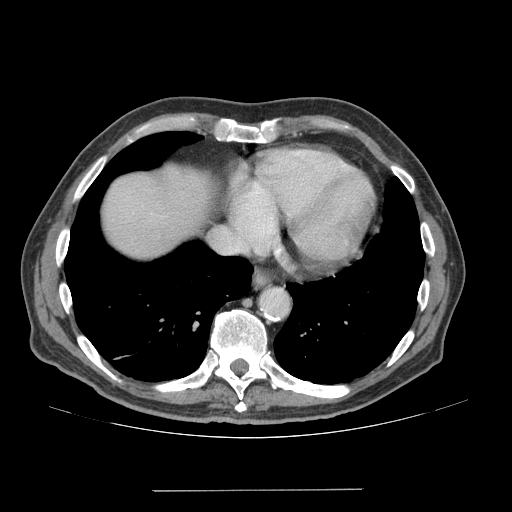
Contrast-enhanced abdominal CT (liver protocol), one axial slice; slice 66 of 77 in the series (ordered by position); 140 kVp; soft-tissue window (W 400 / L 40 HU); 512 × 512 image matrix. From the clinical record (not read from this slice): diagnosis: hepatocellular carcinoma (patient treated with transarterial chemoembolisation; whether this scan precedes or follows treatment is not stated here); TNM stage (as recorded): Stage-IVA; Child-Pugh class: A; tumour differentiation: well differentiated; tumour nodularity: uninodular.
Annotated regions visible in this slice (semi-automatic segmentation, software-assisted and operator-edited):
- abdominal aorta: bounding box (x1, y1, x2, y2) in pixels: (260, 288, 288, 316)
- liver parenchyma outside the tumour (the mass and vessels are separate outlines, so this box may not span the whole liver): (104, 168, 210, 258)